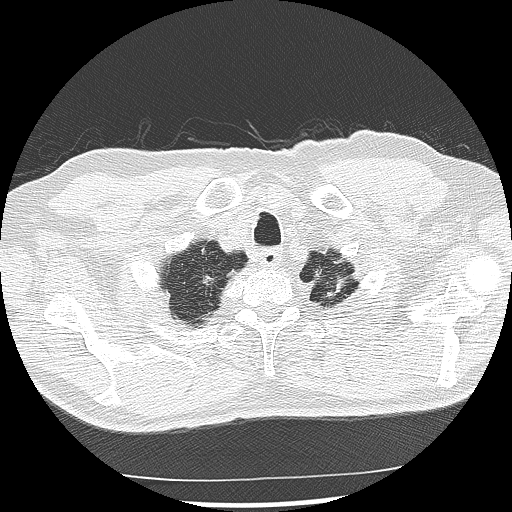
Low-dose screening chest CT, one axial slice. Position 127 of 142 along the scan axis. Reconstruction kernel LUNG. 120 kVp. Lung window (W 1500 / L -600 HU). 2.5 mm slice thickness. 512 × 512 image matrix, field of view 360 × 360 mm.
Outlined on this slice (outlined manually by an expert reader):
- lesion 3 (nodule, upper lobe of right lung): box from (x=203, y=275) to (x=214, y=285) px